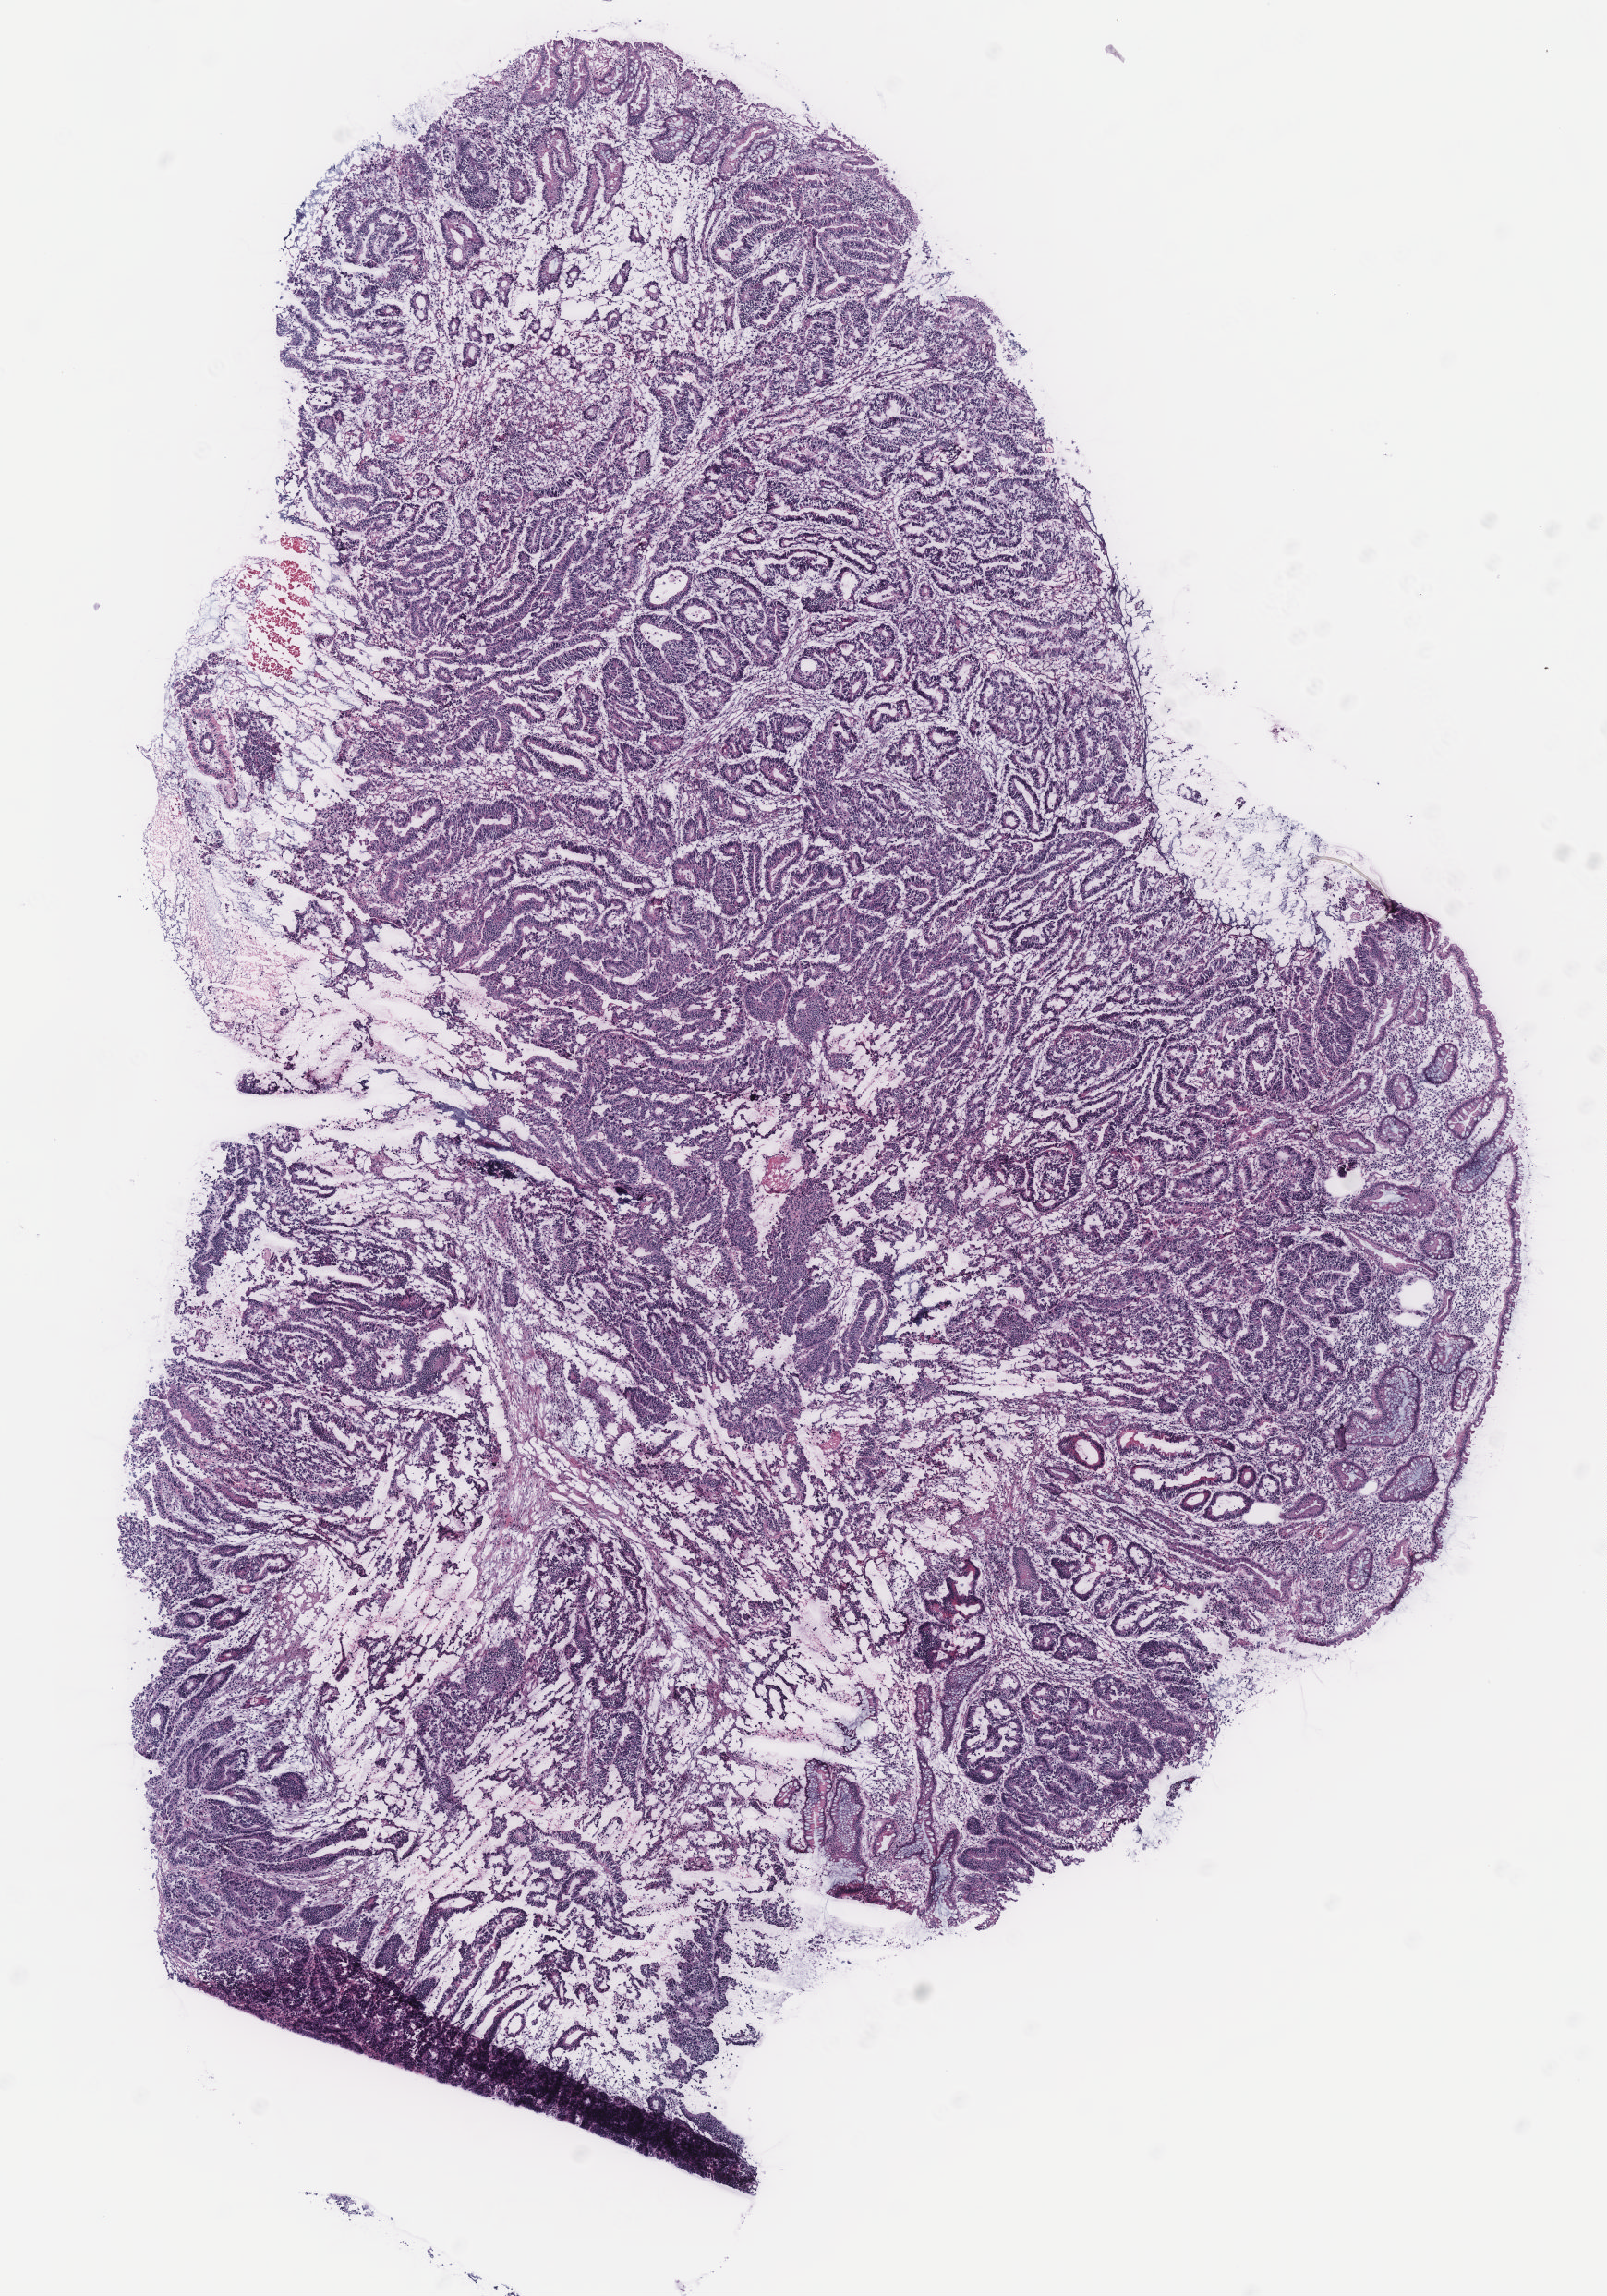
H&E-stained whole-slide image — whole scanned area (about 7.0 x 9.9 mm) shown as a low-resolution overview. Colon, tissue type not recorded. Male patient.
Patient diagnosis: Adenocarcinoma, NOS.